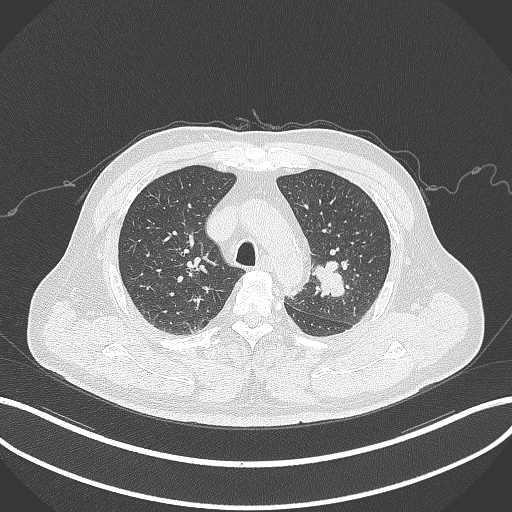
Chest CT, one axial slice; slice 227 of 286 in the series (ordered by position); reconstruction kernel B70f; 120 kVp; lung window (W 1500 / L -600 HU); 1 mm slice thickness; 512 × 512 image matrix, field of view 400 × 400 mm. Patient: male, 67 years. Case-level facts recorded for this patient, not image findings: clinical TNM (as recorded): T2a N1 M0.
Outlined on this slice (bounding box drawn by a radiologist):
- lung tumour (recorded histology: adenocarcinoma): bounding box (x1, y1, x2, y2) in pixels: (310, 257, 350, 301)